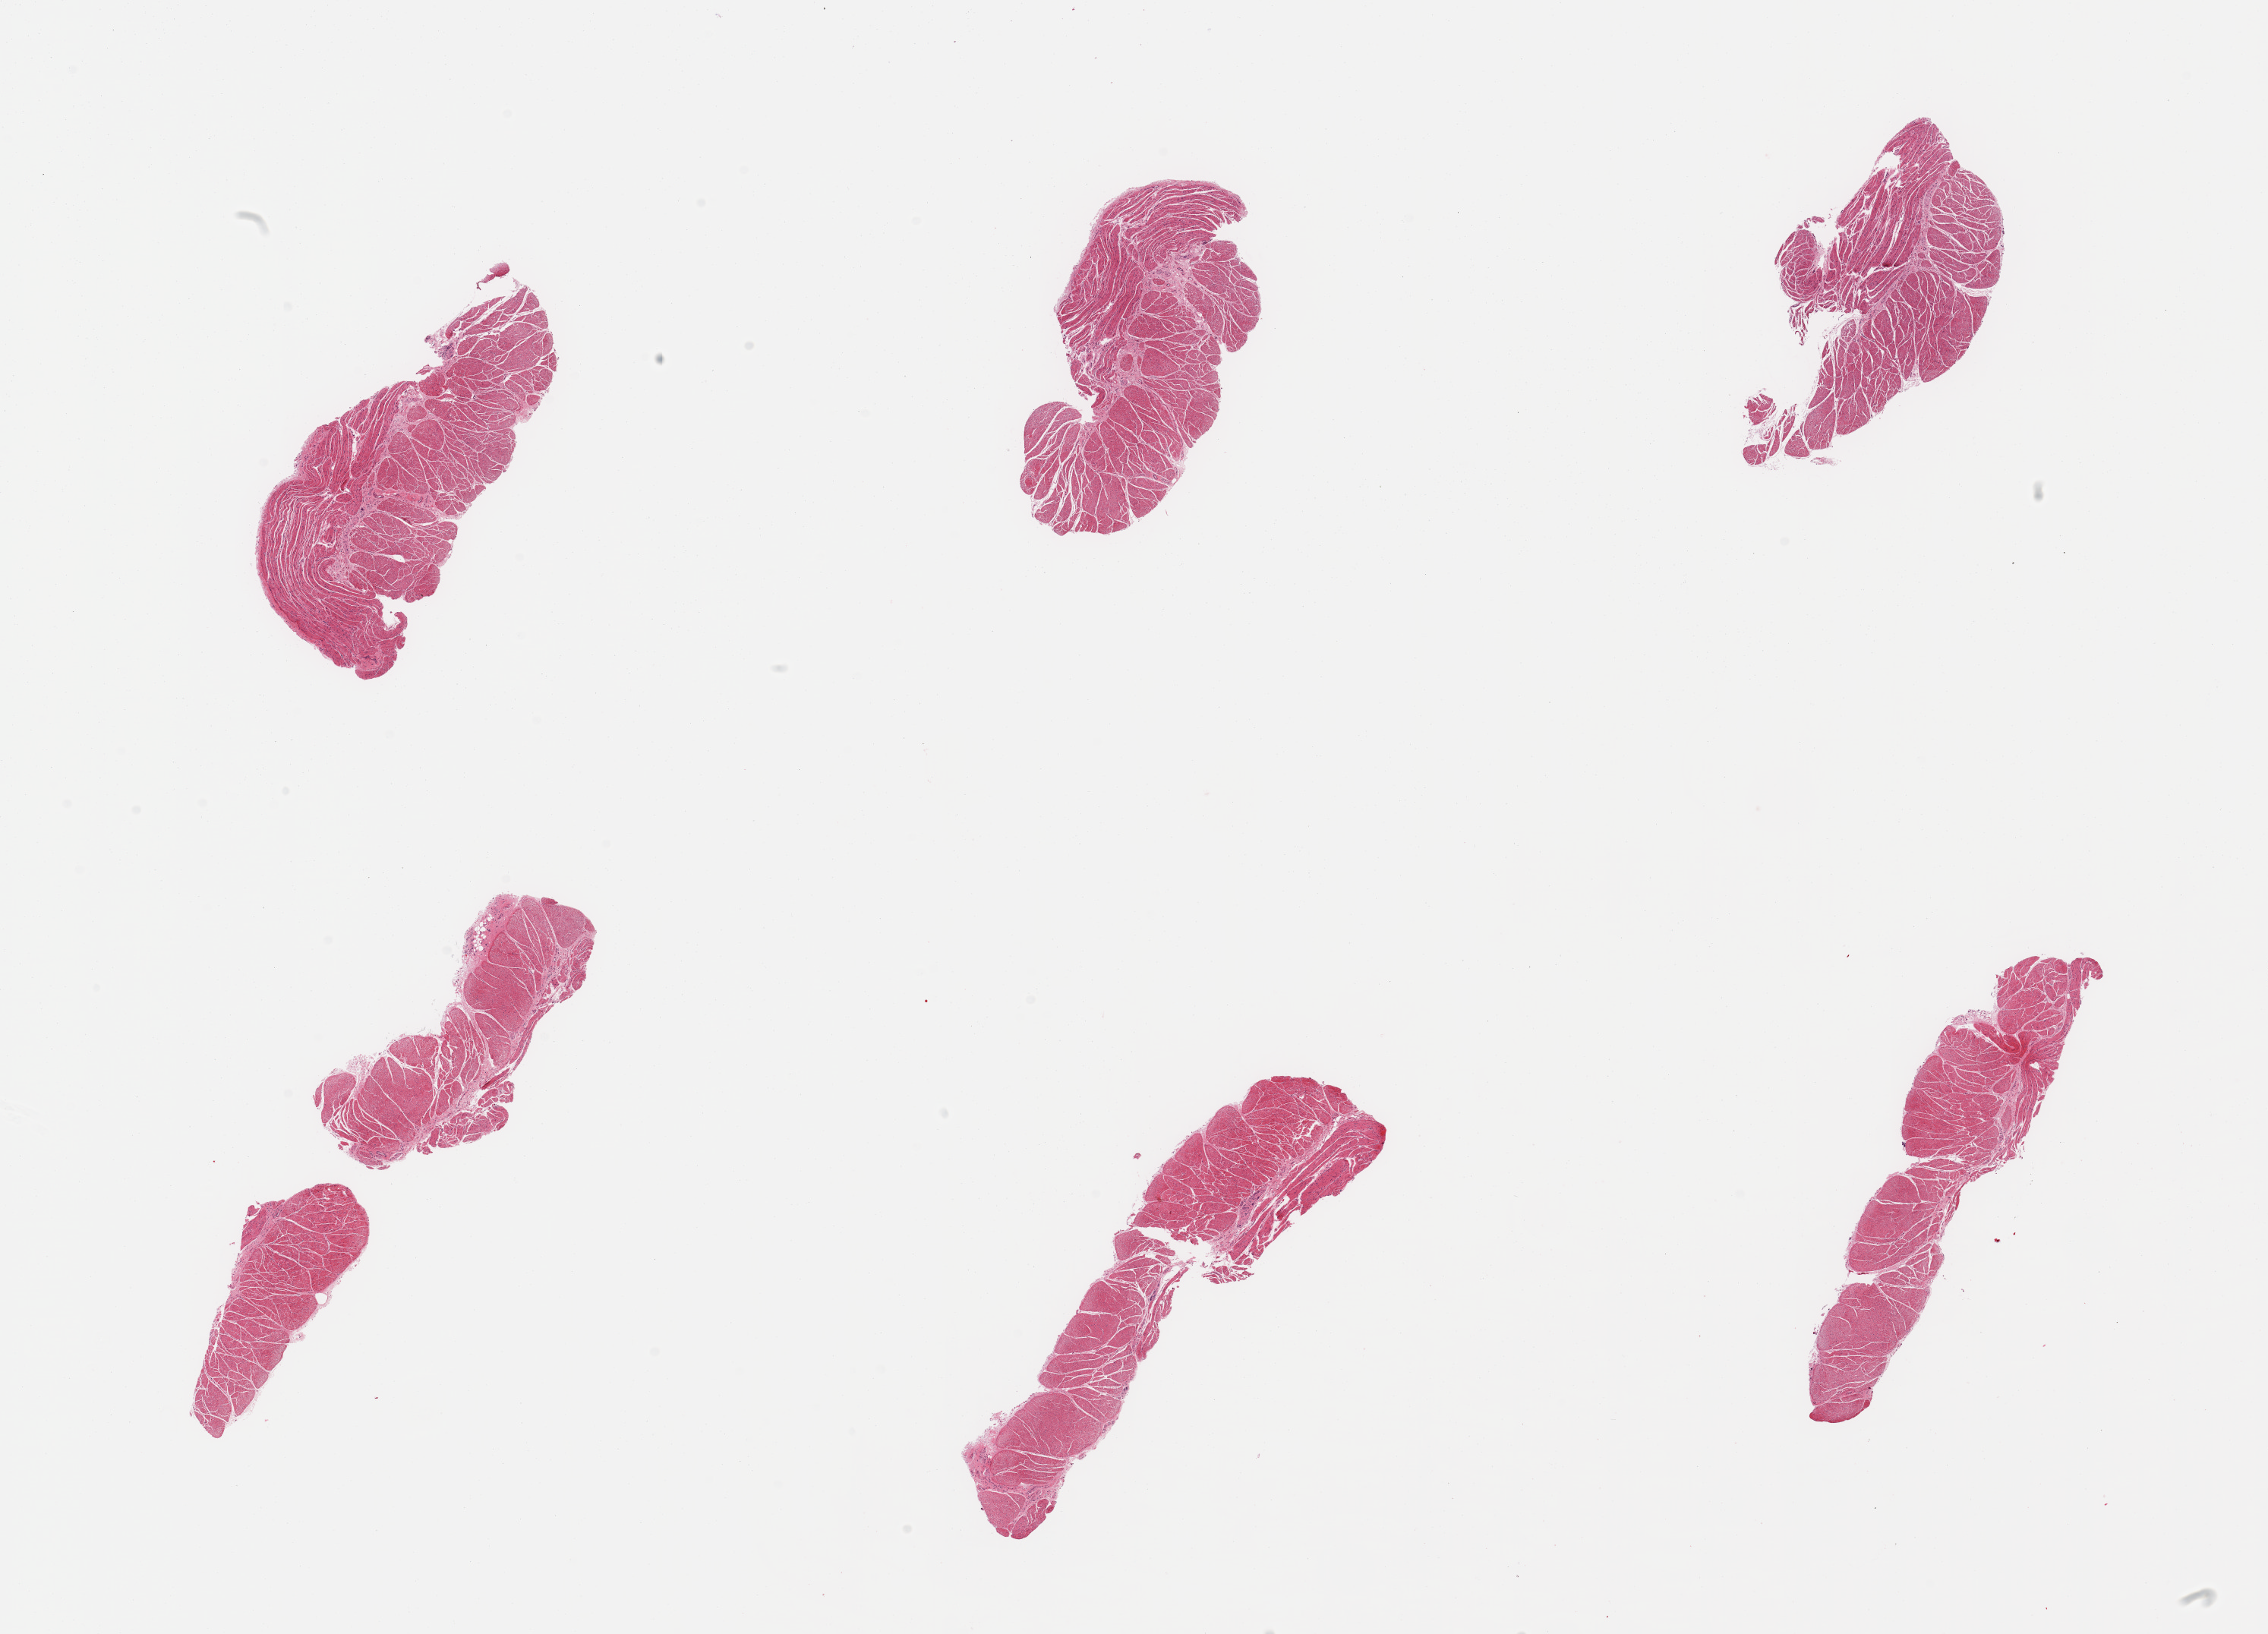
Digitized haematoxylin and eosin-stained section, a low-resolution overview of the entire scanned area, about 23.6 x 17.0 mm (from a 20x scan). PAXgene-fixed paraffin-embedded (PFPE) section. Sampled site (target tissue): esophageal muscle. Donor tissue sample. Donor: male.
* review note (as recorded): 6 pieces, confirmed target muscularis